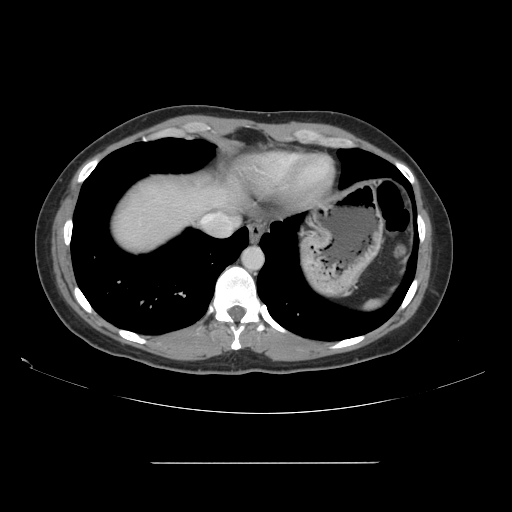
Contrast-enhanced abdominal CT, one axial slice. Slice 138 of 151 in the series (ordered by position). 120 kVp. Intravenous contrast given. Soft-tissue window (W 400 / L 40 HU). 2.5 mm slice thickness. 512 × 512 image matrix. Female patient, age 46 years. From the clinical record (not read from this slice): diagnosis: colorectal cancer liver metastases, imaged before liver resection; multiple liver metastases: yes; largest metastasis: 3 cm.
Annotated regions visible in this slice (expert manual segmentation):
- hepatic veins: box from (x=202, y=214) to (x=219, y=224) px
- liver: (x=112, y=178)–(x=235, y=252)
- planned liver remnant (the part of the liver to remain after resection): (x=127, y=179)–(x=235, y=227)